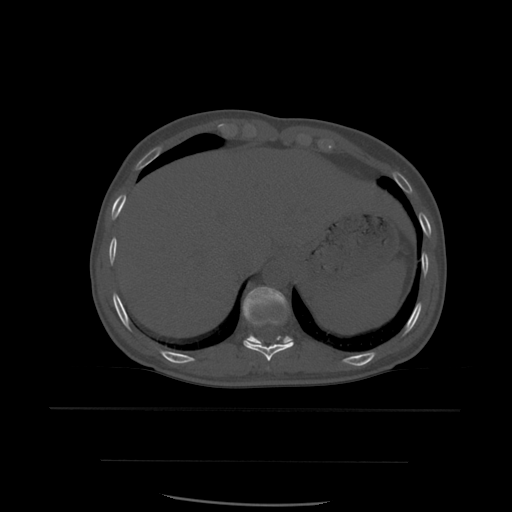
CT including the spine, one axial slice. Position 309 of 574 along the scan axis. Bone window (W 1800 / L 400 HU). 1.25 mm slice thickness. 512 × 512 image matrix, field of view 392 × 392 mm. Patient age 48 years. Case-level facts recorded for this patient, not image findings: primary cancer: lung; vertebrae with lytic lesions (as recorded): T11.
Outlined on this slice (semi-automatically segmented with operator editing):
- T10 vertebra: bounding box <243,318,294,361> (left, top, right, bottom; pixels)
- T11 vertebra: <243,287,293,346>